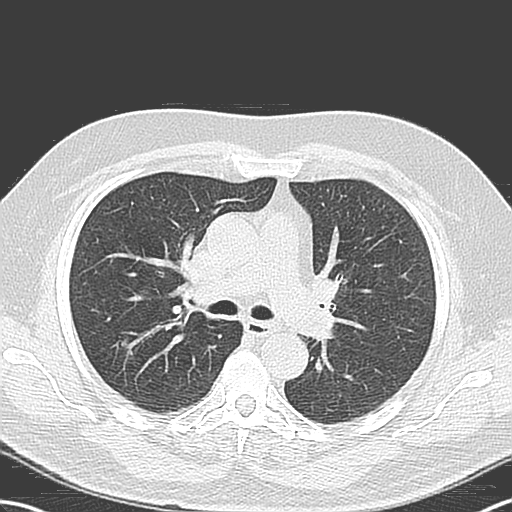
Low-dose screening chest CT, one axial slice; position 76 of 131 along the scan axis; 120 kVp; lung window (W 1500 / L -600 HU); 512 × 512 image matrix, field of view 356 × 356 mm.
Structures marked on this image (outlined manually by an expert reader):
- lesion 1 (tumor, upper lobe of right lung): bounding box [x1, y1, x2, y2] px = [121, 341, 127, 346]